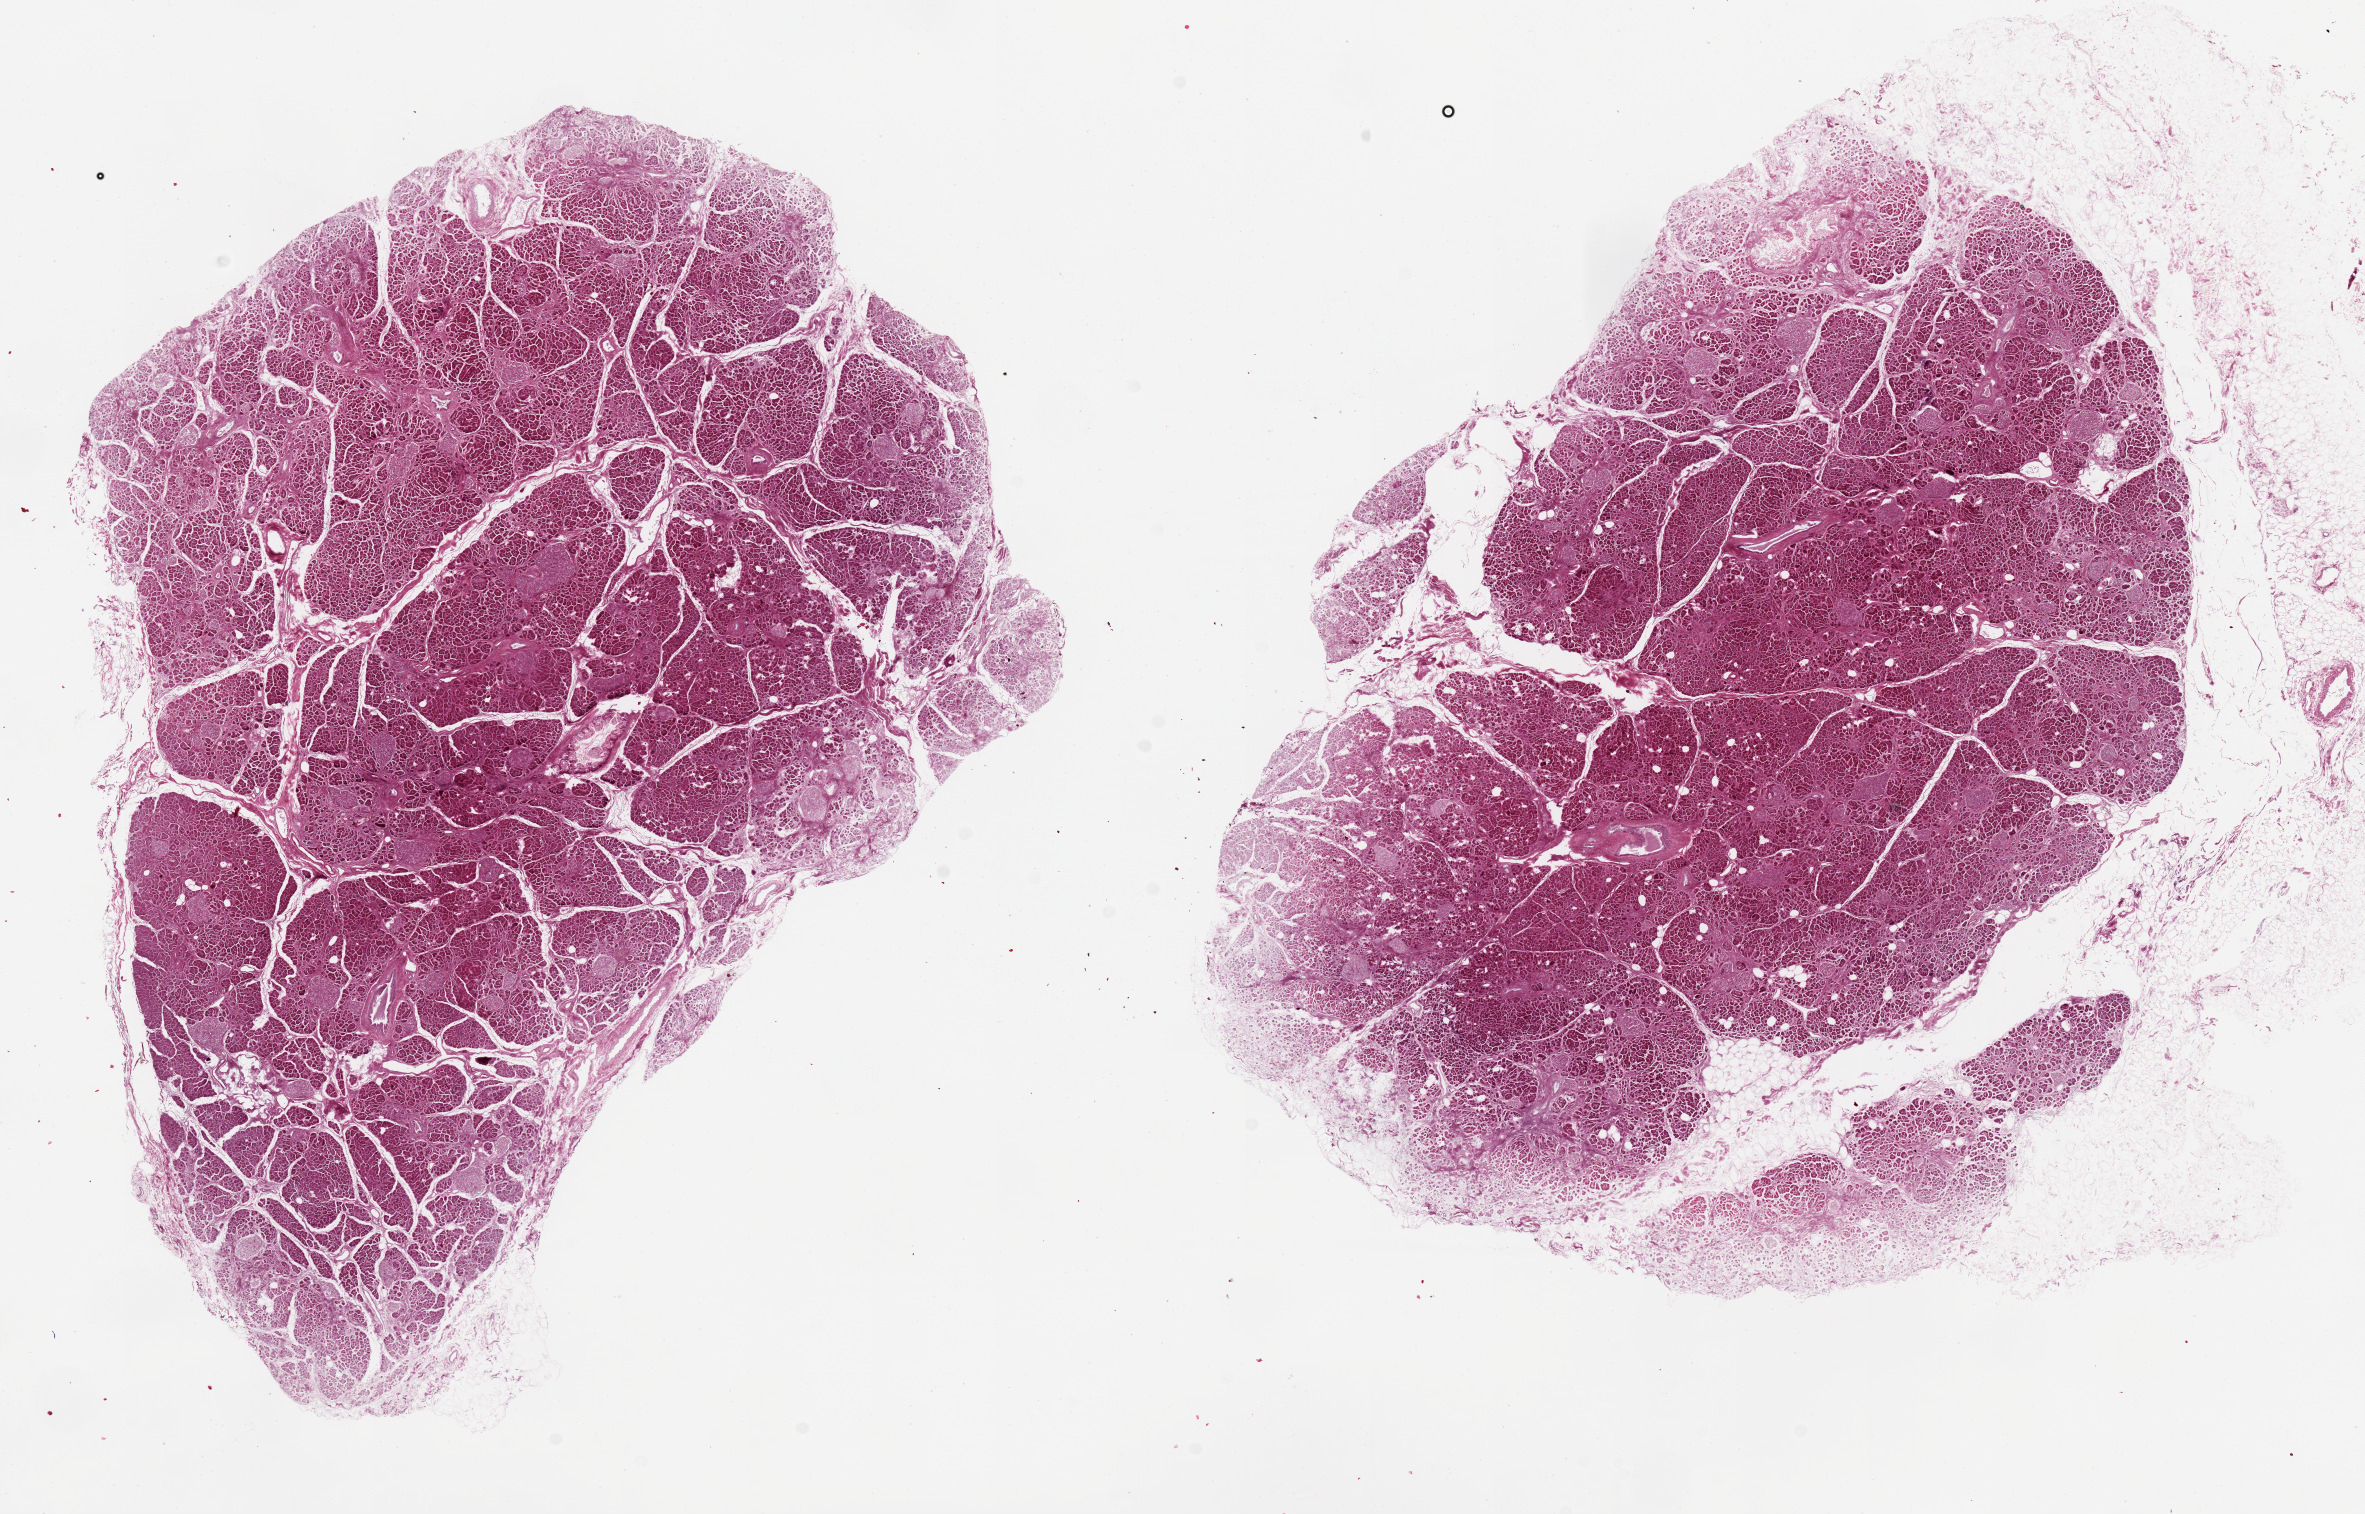
Whole-slide image, hematoxylin and eosin (H&E) stain, shown as a low-resolution overview of the whole scanned area (about 18.7 x 12.0 mm, slide scanned at 20x), PAXgene-fixed paraffin-embedded (PFPE) section, section of pancreas (target tissue), donor tissue sample. Donor: female.
- review note (as recorded): 2 pieces 11x9 & 9x6 mm; 2 mm saponified adipose along edge of one piece